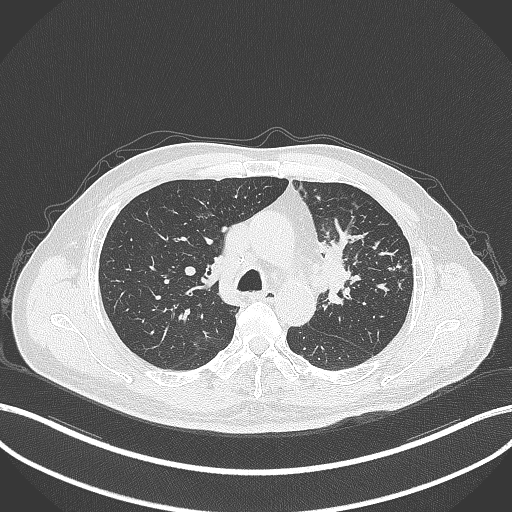
Chest CT, one axial slice. Slice 237 of 386 in the series (ordered by position). 120 kVp. Lung window (W 1500 / L -600 HU). 1 mm slice thickness. 512 × 512 image matrix, field of view 400 × 400 mm. Patient: male, 69 years. Case-level facts recorded for this patient, not image findings: clinical TNM (as recorded): T2a N2 M0; histopathological grade: G2-3.
Outlined on this slice (bounding box drawn by a radiologist):
- lung tumour (recorded histology: adenocarcinoma): bounding box (x1, y1, x2, y2) in pixels: (319, 230, 358, 307)